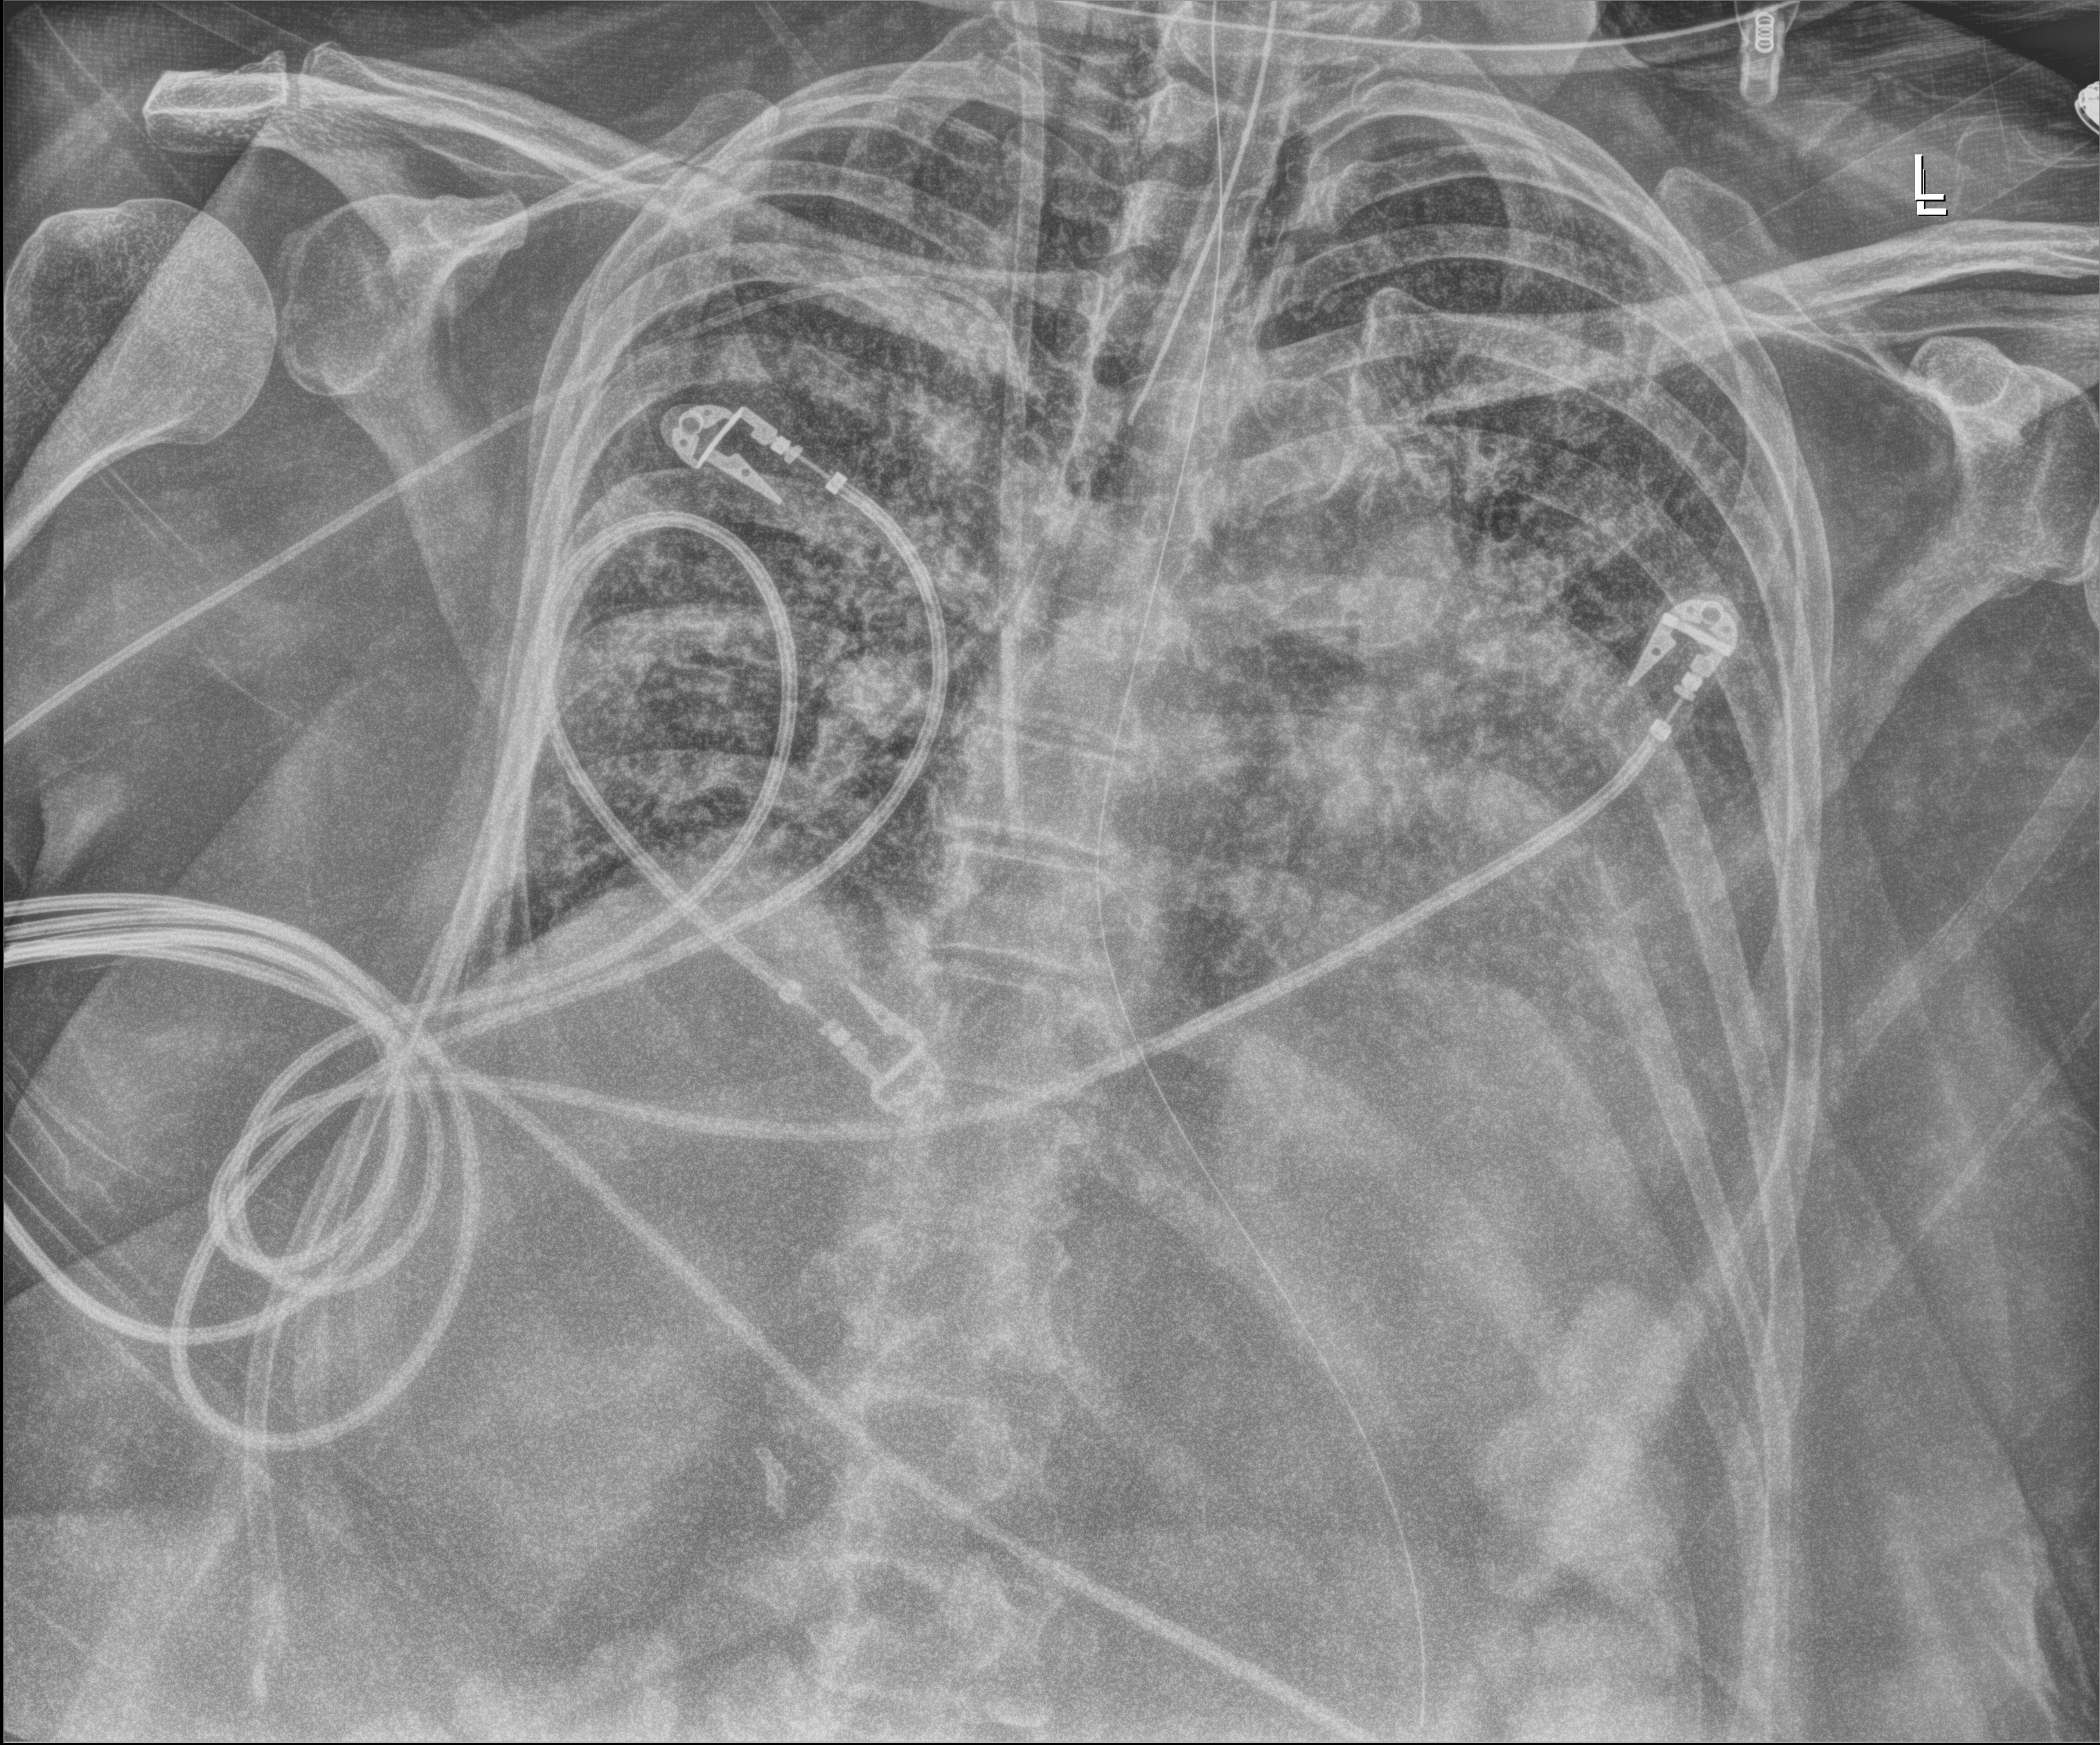
Chest radiograph (digital radiography), anteroposterior (AP) projection. Patient hospitalised with COVID-19; female, aged 60–74 years.
From the hospital-stay record, not from the radiograph (when in the stay this image was taken is not recorded): mechanically ventilated during this hospital stay: yes; admitted to intensive care during this hospital stay: yes.